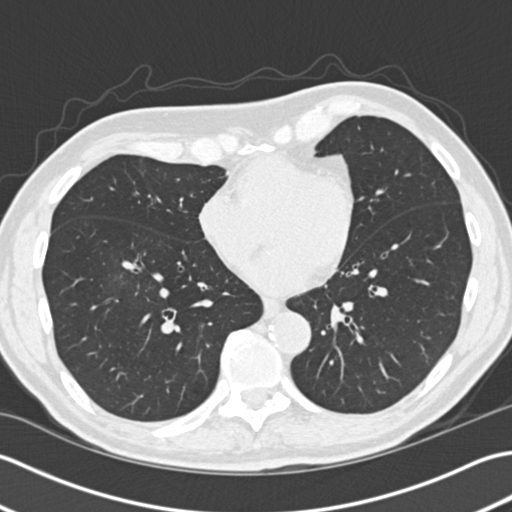
Low-dose screening chest CT, one axial slice; slice 64 of 172 in the series (ordered by position); reconstruction kernel B30f; 120 kVp; lung window (W 1500 / L -600 HU); 2 mm slice thickness; 512 × 512 image matrix, field of view 350 × 350 mm.
Structures marked on this image (manually delineated by an expert):
- lesion 1 (tumor, lower lobe of right lung): bounding box <122,261,141,272> (left, top, right, bottom; pixels)